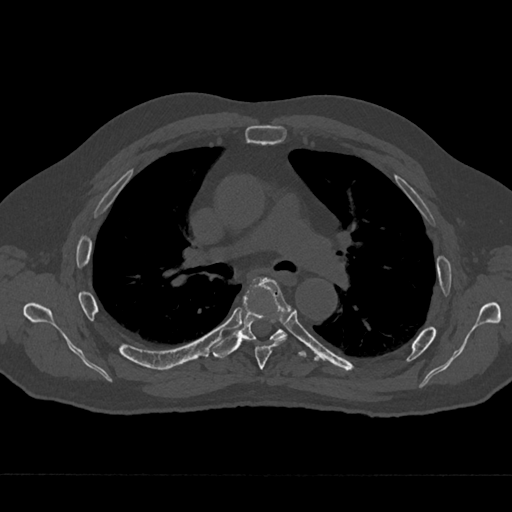
CT including the spine, one axial slice. Position 450 of 797 along the scan axis. Reconstruction kernel Br40s/3. 120 kVp. Bone window (W 1800 / L 400 HU). 512 × 512 image matrix. Patient: male, 75 years. From the clinical record (not read from this slice): primary cancer: renal.
Structures marked on this image (semi-automatically segmented with operator editing):
- T5 vertebra: box from (x=255, y=279) to (x=291, y=370) px
- T6 vertebra: (x=211, y=277)–(x=306, y=358)